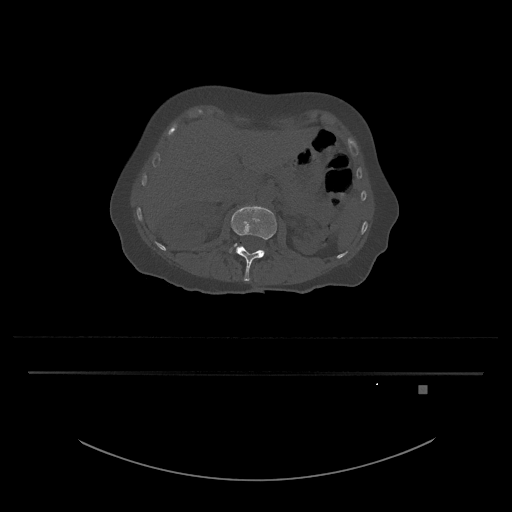
CT including the spine, one axial slice; slice 482 of 797 in the series (ordered by position); 120 kVp; bone window (W 1800 / L 400 HU); 0.5 mm slice thickness; 512 × 512 image matrix, field of view 500 × 500 mm. Patient: female, 57 years. From the clinical record (not read from this slice): primary cancer: cervical.
Outlined on this slice (semi-automatic segmentation, software-assisted and operator-edited):
- L3 vertebra: bounding box <229,243,237,253> (left, top, right, bottom; pixels)